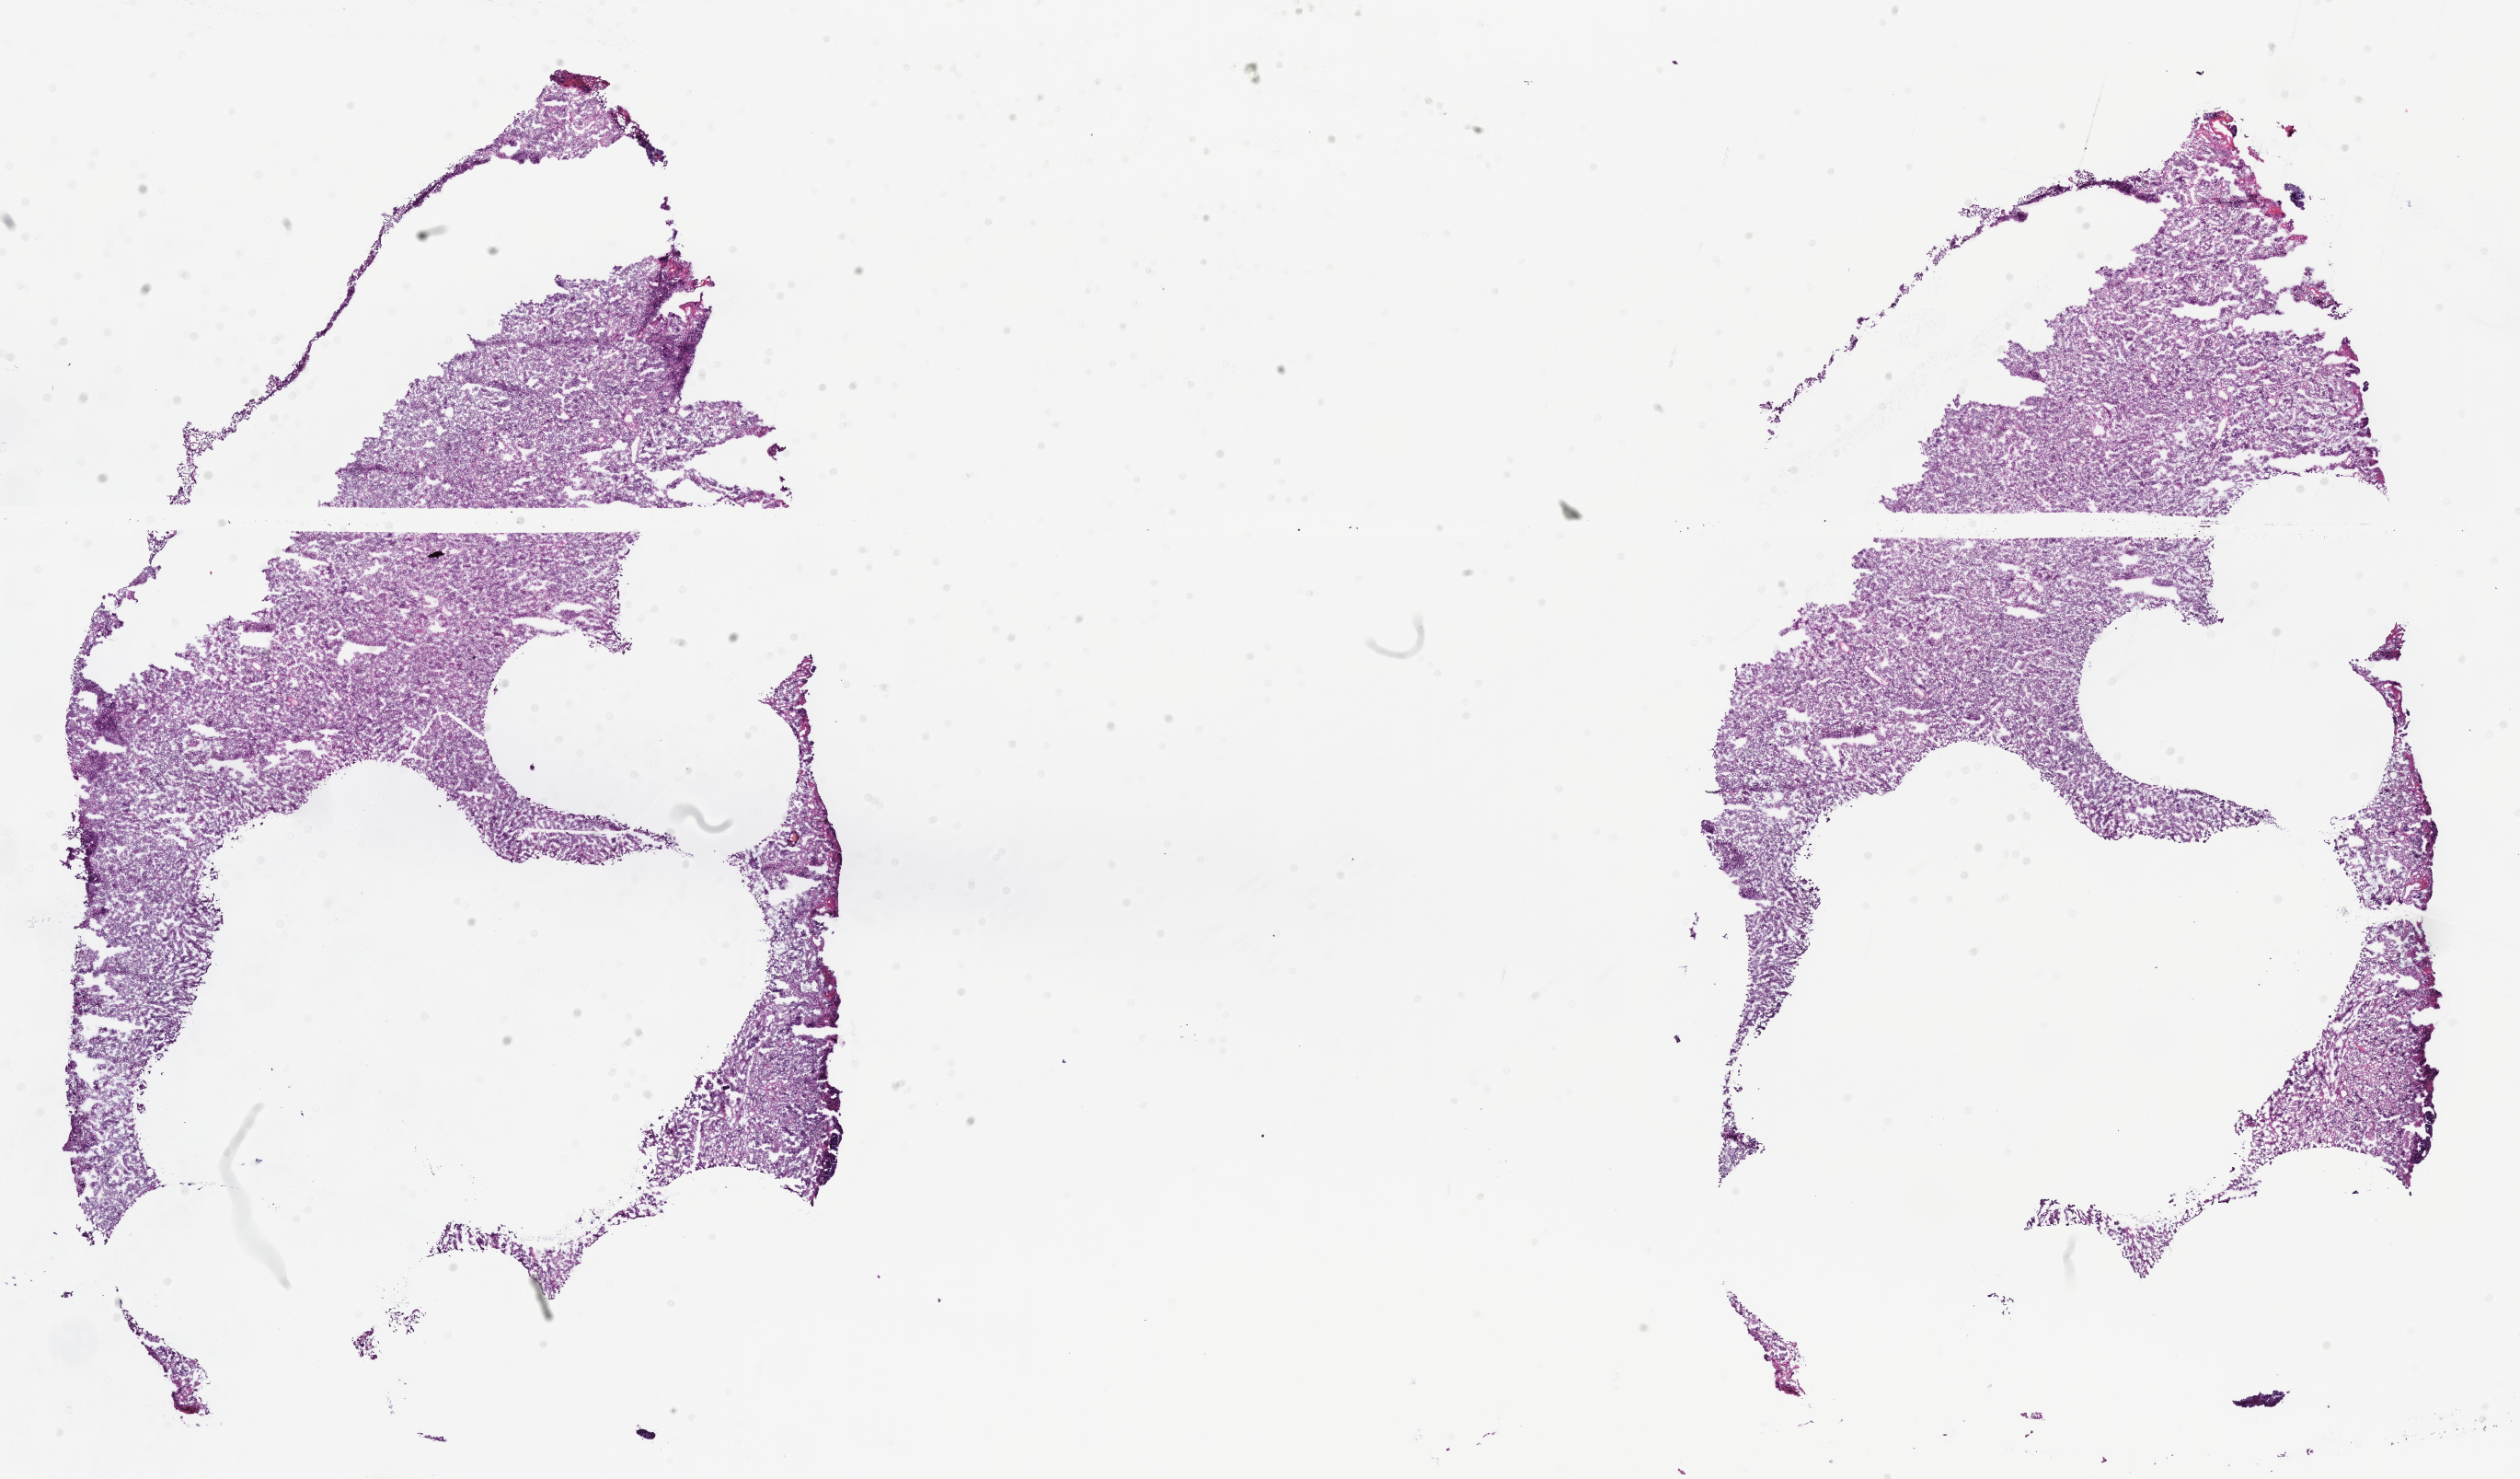
H&E whole-slide image — shown as a low-resolution overview of the whole scanned area (about 22.1 x 13.0 mm); frozen section (tissue freezing medium); primary tumor; site: transverse colon. Female patient; age at initial diagnosis 58 years. Tumor grade: G4 (undifferentiated). Slide review estimates, as recorded: tumor cells 70%, tumor nuclei 70%, stromal cells 5%, necrosis 0%, normal cells 25%. Infiltration values recorded for this section: lymphocyte infiltration 10%, monocyte infiltration 2%, neutrophil infiltration 10%.
AJCC pathologic stage: Stage IIB. Diagnosis: Adenocarcinoma, metastatic, NOS.